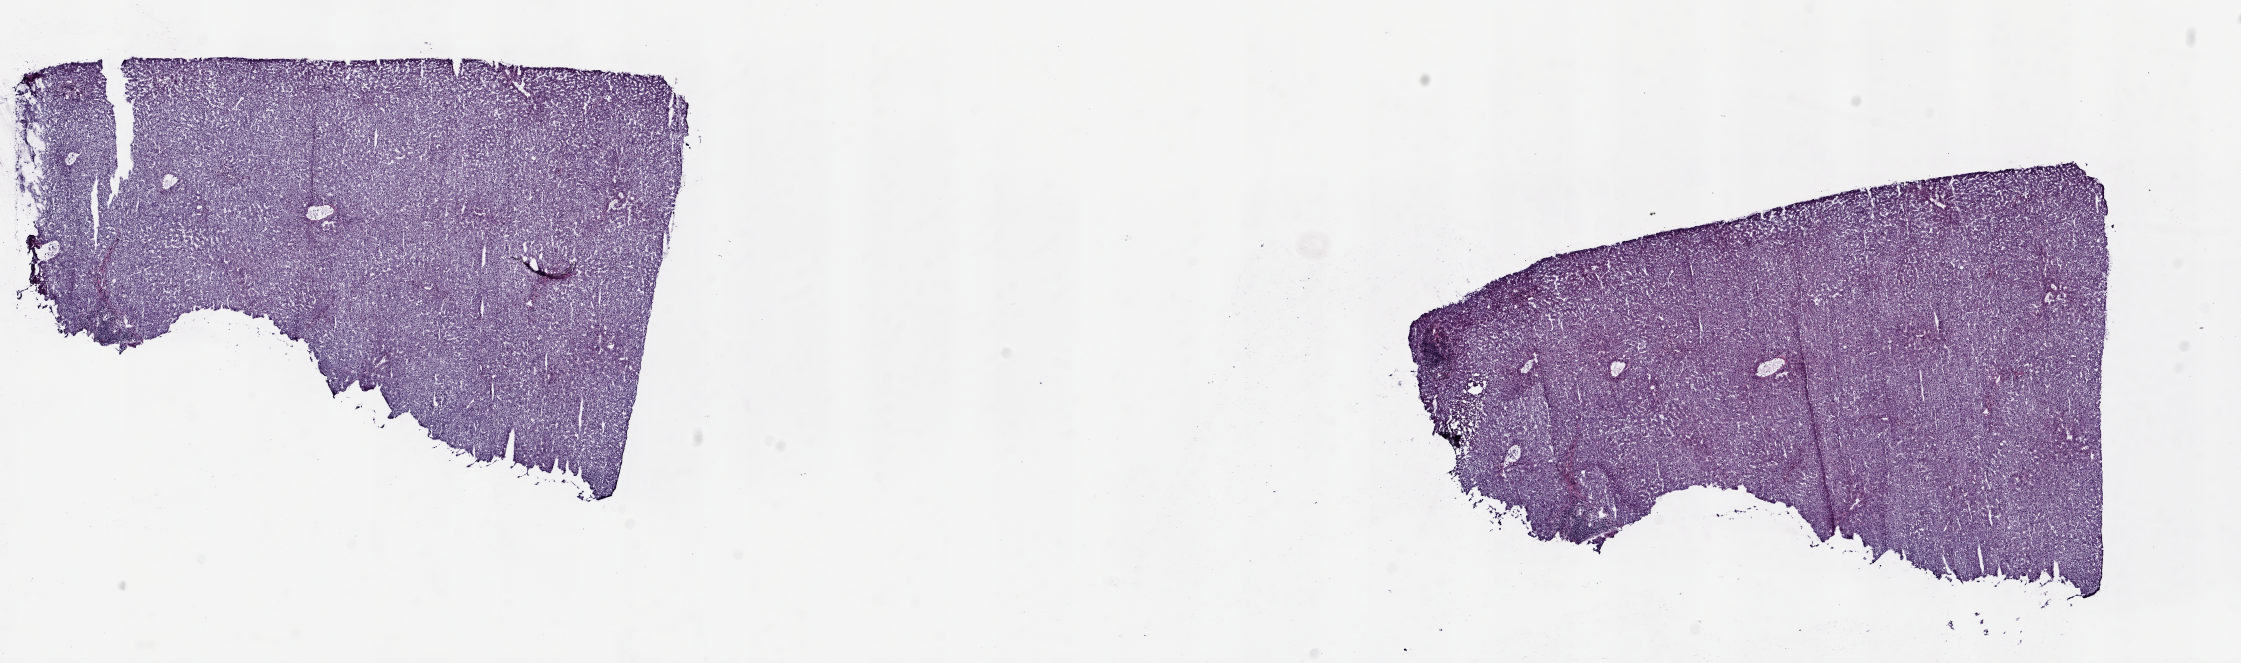
Whole-slide histology image, H&E-stained, a low-resolution overview of the entire scanned area, about 17.8 x 5.3 mm, frozen section, sample: solid tissue normal (non-tumour tissue), liver. Female patient; age at initial diagnosis 57 years. Composition of this section per pathologist review: tumour cells 0%, tumour nuclei 0%, normal cells 80%, stromal cells 20%, necrosis 0%. Infiltration values recorded for this section: lymphocyte infiltration 7%, monocyte infiltration 0%, neutrophil infiltration 0%.
This section: solid tissue normal (non-tumour) sample from the same patient. Patient diagnosis: Hepatocellular carcinoma, NOS.